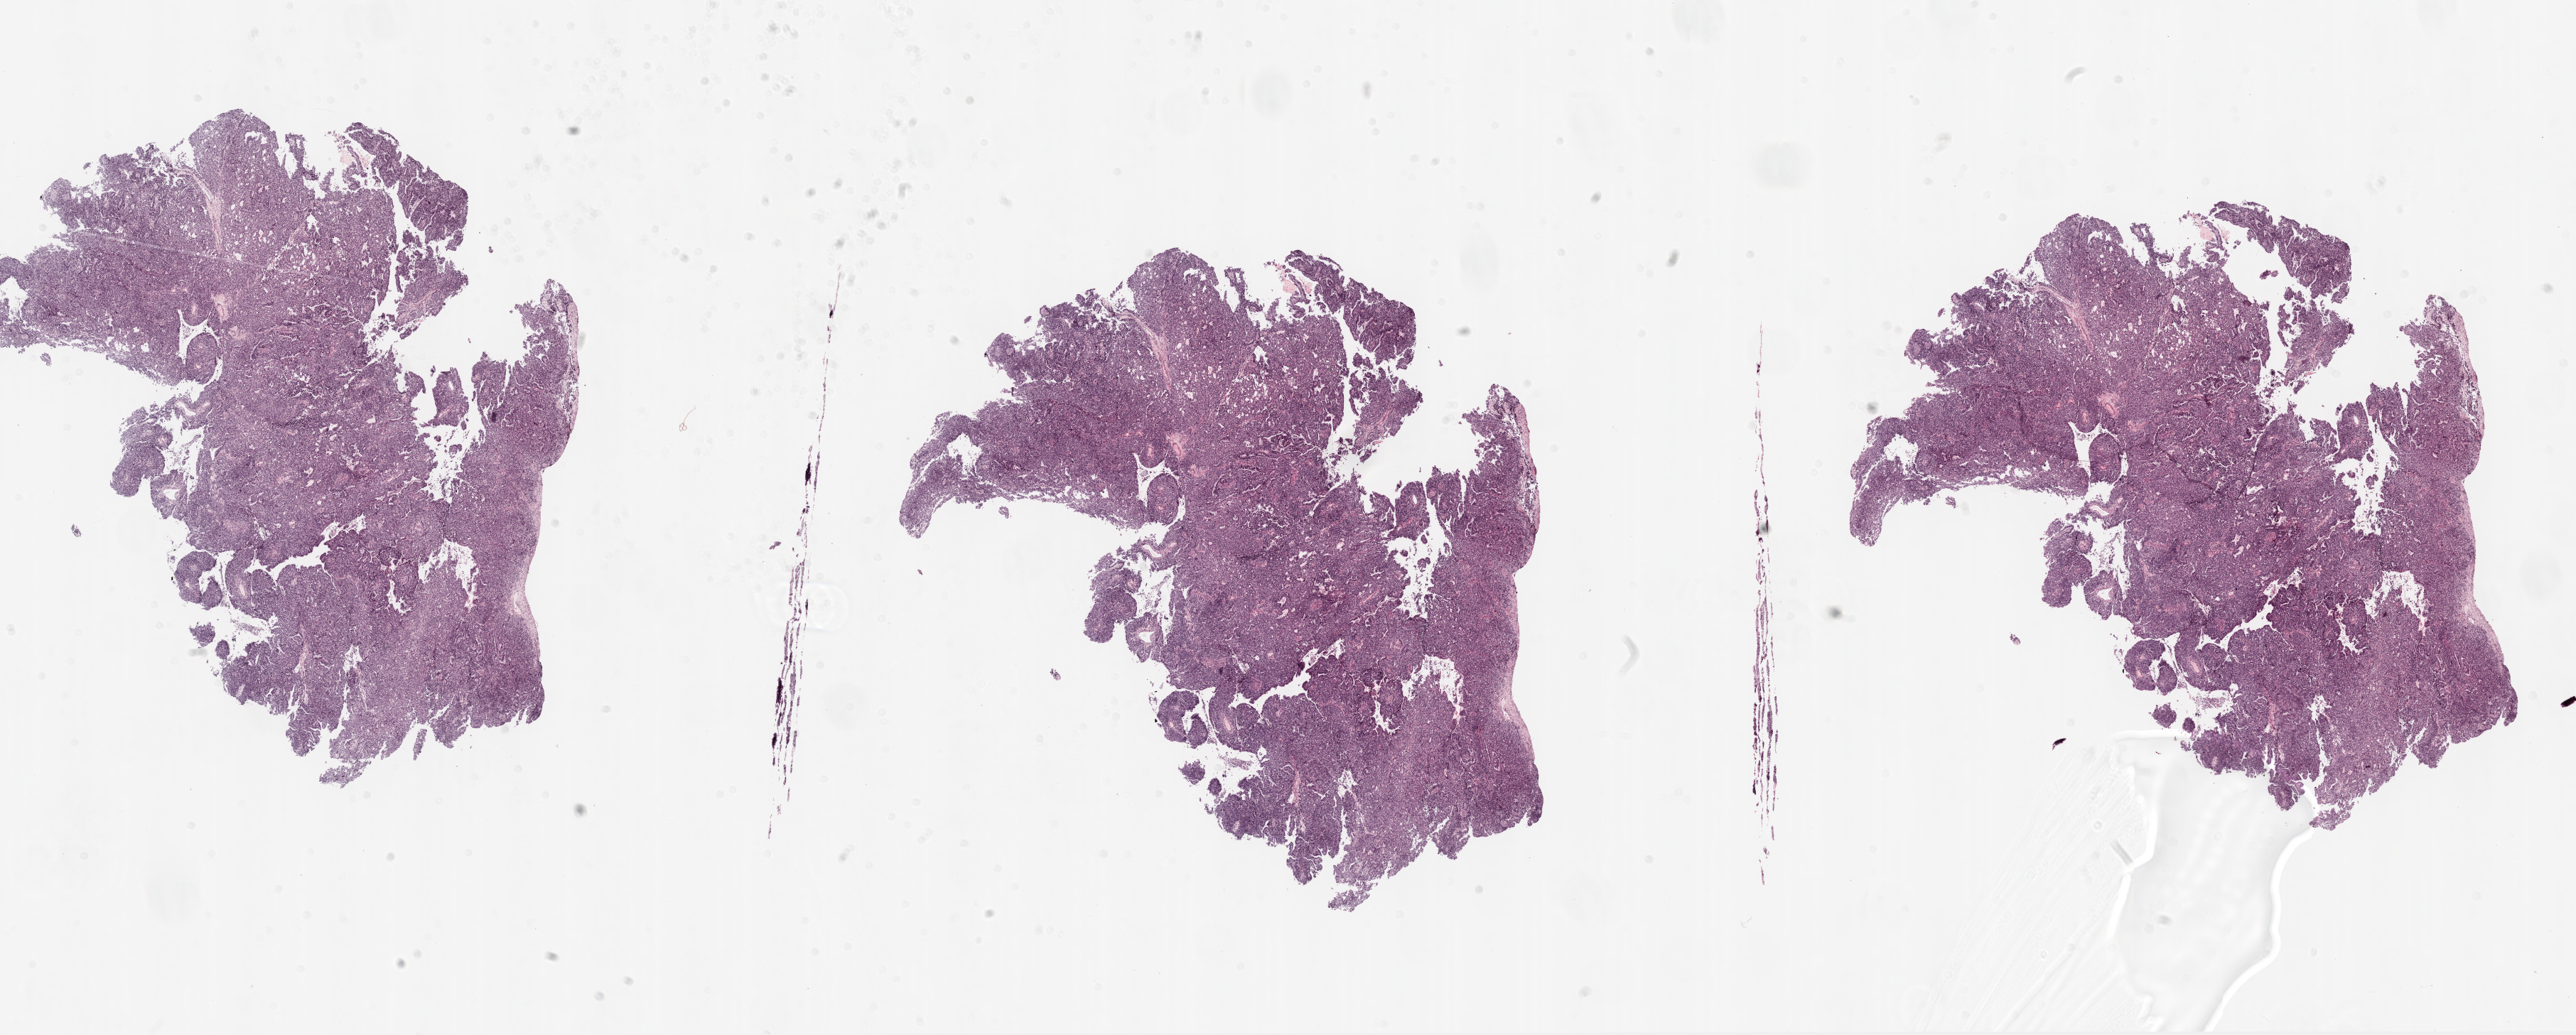
Hematoxylin and eosin (H&E) stained whole-slide image, shown as a low-resolution overview of the whole scanned area (about 29.1 x 11.7 mm, slide scanned at 20x), frozen section from the top of the tissue portion, sample: primary tumour, ovary. Female, age 58 years at initial diagnosis. Histologic grade: G3 (poorly differentiated). Pathologist review of this section (percent, as recorded): tumour cells 90%, tumour nuclei 90%, normal cells 0%, stromal cells 10%, necrosis 0%. Inflammatory infiltration, as recorded: lymphocyte infiltration 0%, monocyte infiltration 0%, neutrophil infiltration 0%.
• FIGO stage: IIIC
• pathologic diagnosis: Serous cystadenocarcinoma, NOS
• laterality: bilateral